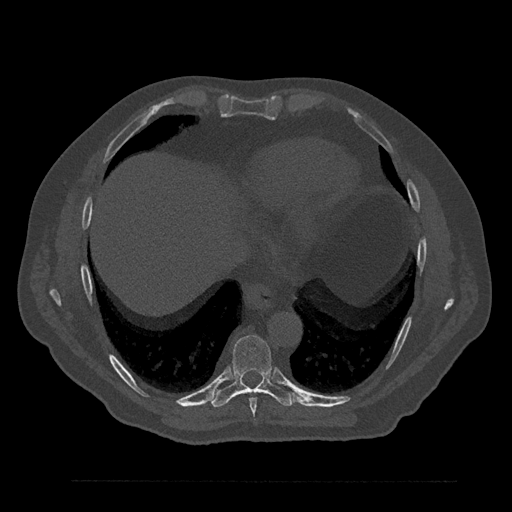
CT including the spine, one axial slice. Slice 419 of 797 in the series (ordered by position). Reconstruction kernel Br40s/3. 120 kVp. Bone window (W 1800 / L 400 HU). 0.5 mm slice thickness. 512 × 512 image matrix. Patient: male, 61 years. Case-level facts recorded for this patient, not image findings: primary cancer: prostate.
Annotated regions visible in this slice (semi-automatic segmentation, software-assisted and operator-edited):
- T8 vertebra: bounding box [x1, y1, x2, y2] px = [249, 397, 257, 416]
- T9 vertebra: [211, 335, 296, 408]